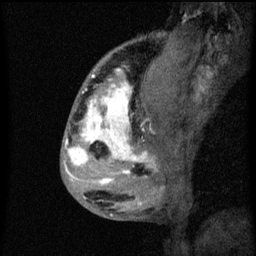
Breast MRI (dynamic contrast-enhanced), one sagittal slice; position 22 of 60 along the scan axis; dynamic contrast-enhanced series, image 2 of 3 at this slice position (ordered by acquisition); 1.5 T; TE 4.2 ms, TR 8 ms; 2 mm slice thickness; 256 × 256 image matrix. Female patient, age 50 years.
Structures marked on this image (semi-automatic segmentation, software-assisted and operator-edited):
- analysis volume of interest (the breast-tissue region the enhancement analysis was run in; not a lesion): bounding box (x1, y1, x2, y2) in pixels: (66, 64, 141, 187)
- tumour enhancement mask (voxels above the 70 % enhancement threshold inside the analysis volume of interest): (66, 68, 141, 185)